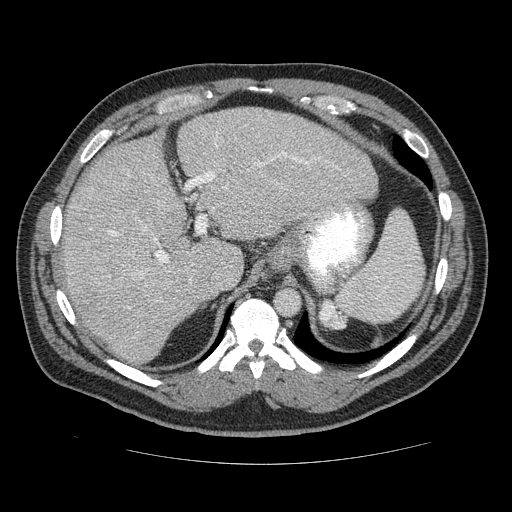
Contrast-enhanced abdominal CT (liver protocol), one axial slice; 120 kVp; soft-tissue window (W 400 / L 40 HU); 2.5 mm slice thickness; 512 × 512 image matrix. Case-level facts recorded for this patient, not image findings: diagnosis: hepatocellular carcinoma (patient treated with transarterial chemoembolisation; whether this scan precedes or follows treatment is not stated here); TNM stage (as recorded): Stage-II; Child-Pugh class: B.
Outlined on this slice (semi-automatic segmentation, software-assisted and operator-edited):
- liver parenchyma outside the tumour (the mass and vessels are separate outlines, so this box may not span the whole liver): bounding box <52,108,380,364> (left, top, right, bottom; pixels)
- mass: <93,249,178,303>
- liver vessels: <87,144,309,276>